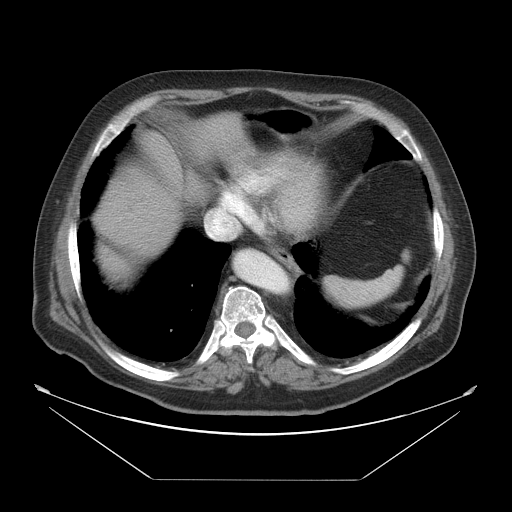
Contrast-enhanced abdominal CT, one axial slice; position 43 of 45 along the scan axis; reconstruction kernel STANDARD; 120 kVp; intravenous contrast given; soft-tissue window (W 400 / L 40 HU); 5 mm slice thickness; 512 × 512 image matrix, field of view 463 × 463 mm. Male patient, age 87 years. Case-level facts recorded for this patient, not image findings: diagnosis: colorectal cancer liver metastases, imaged before liver resection; multiple liver metastases: no; largest metastasis: 4.5 cm; disease in both lobes: yes.
Structures marked on this image (expert manual segmentation):
- liver: bounding box <94,115,250,288> (left, top, right, bottom; pixels)
- planned liver remnant (the part of the liver to remain after resection): <133,115,251,207>